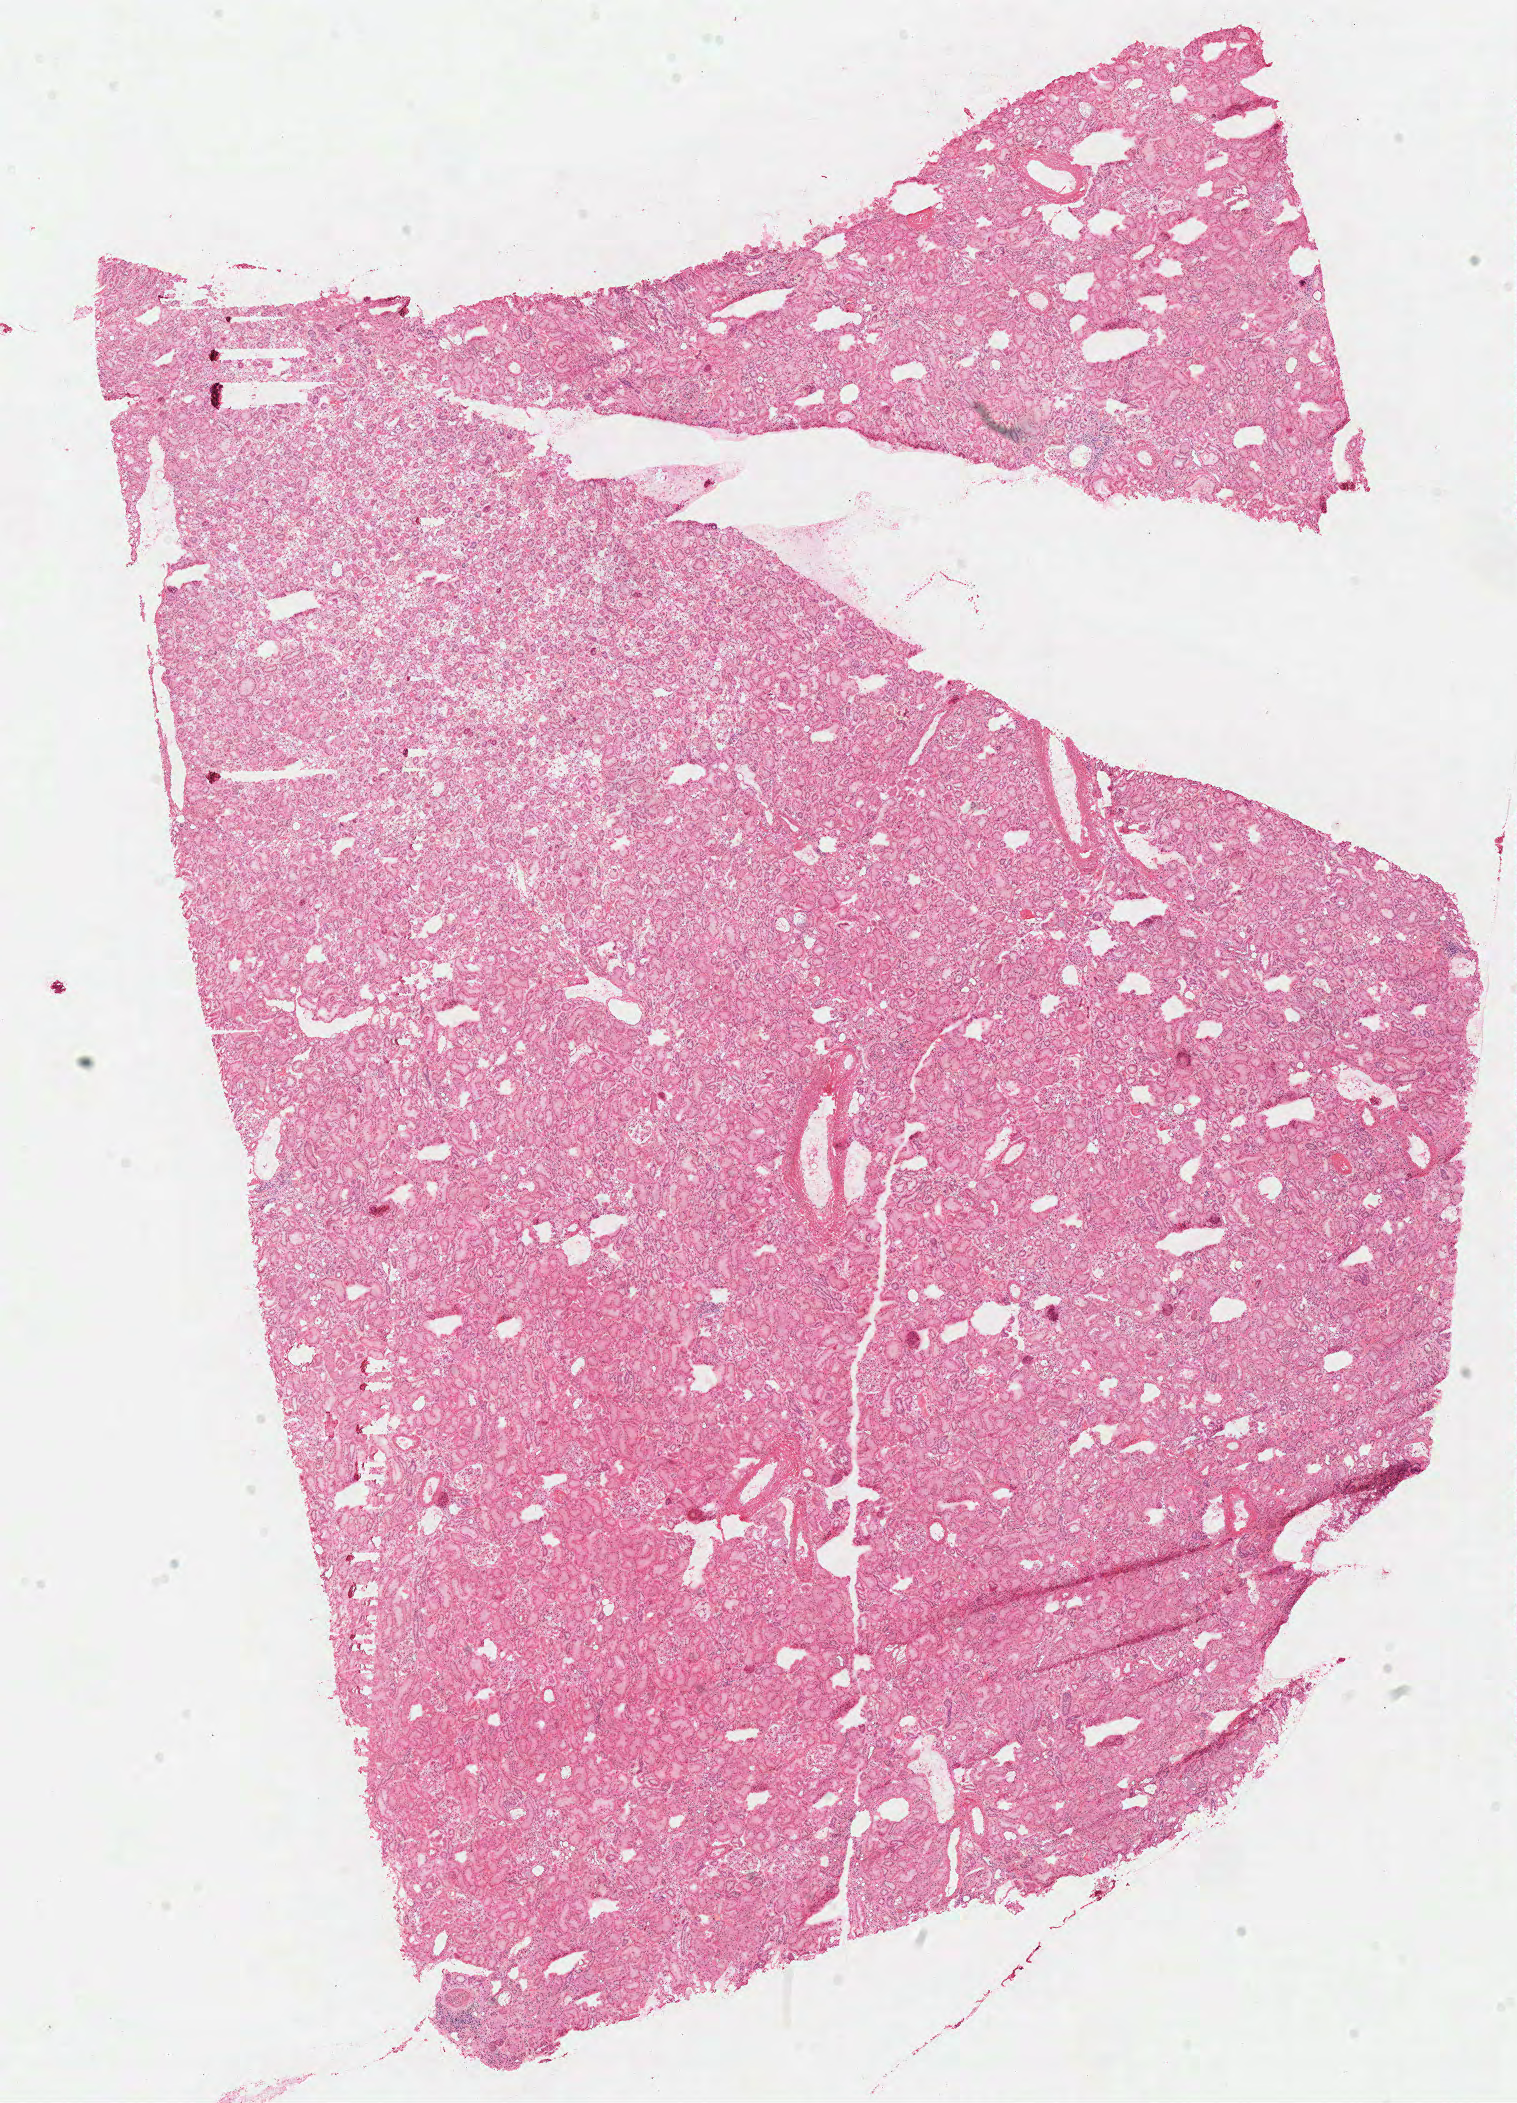
Whole-slide histology image, Hematoxylin and eosin (H&E) stained, a low-resolution overview of the entire scanned area, about 12.0 x 16.6 mm (acquisition: 40x scan). Frozen section. Kidney, solid tissue normal (non-tumour tissue) sample. Patient: male, age at initial diagnosis 63 years.
This section: solid tissue normal (non-tumour) sample from the same patient. Patient diagnosis: Papillary adenocarcinoma, NOS.